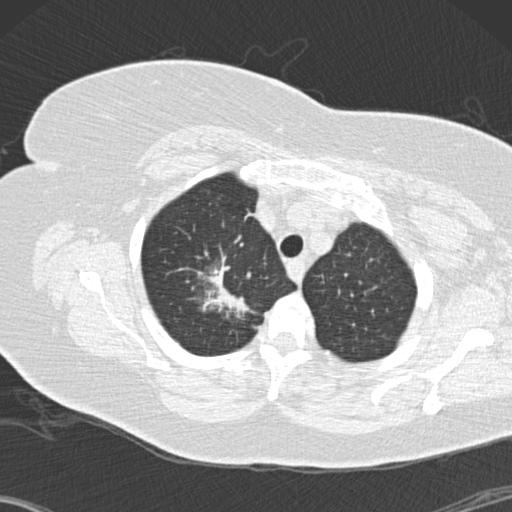
Low-dose screening chest CT, one axial slice. Slice 121 of 146 in the series (ordered by position). 120 kVp. Lung window (W 1500 / L -600 HU). 2 mm slice thickness. 512 × 512 image matrix.
Annotated regions visible in this slice (expert manual segmentation):
- lesion 1 (tumor, upper lobe of right lung): box from (x=202, y=256) to (x=253, y=317) px